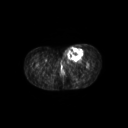
FDG PET of an extremity soft-tissue mass (from a PET/CT study), one axial slice. 3.27 mm slice thickness. 128 × 128 image matrix, field of view 600 × 600 mm. Female patient, age 24 years. Case-level facts recorded for this patient, not image findings: histological type: leiomyosarcoma; grade: high; site of the primary tumour: groin.
Outlined on this slice (expert contour drawn on MRI and transferred to this co-registered scan by the dataset authors):
- gross tumour volume including surrounding oedema: bounding box [x1, y1, x2, y2] px = [62, 44, 83, 62]
- gross tumour volume (mass): [67, 47, 83, 60]